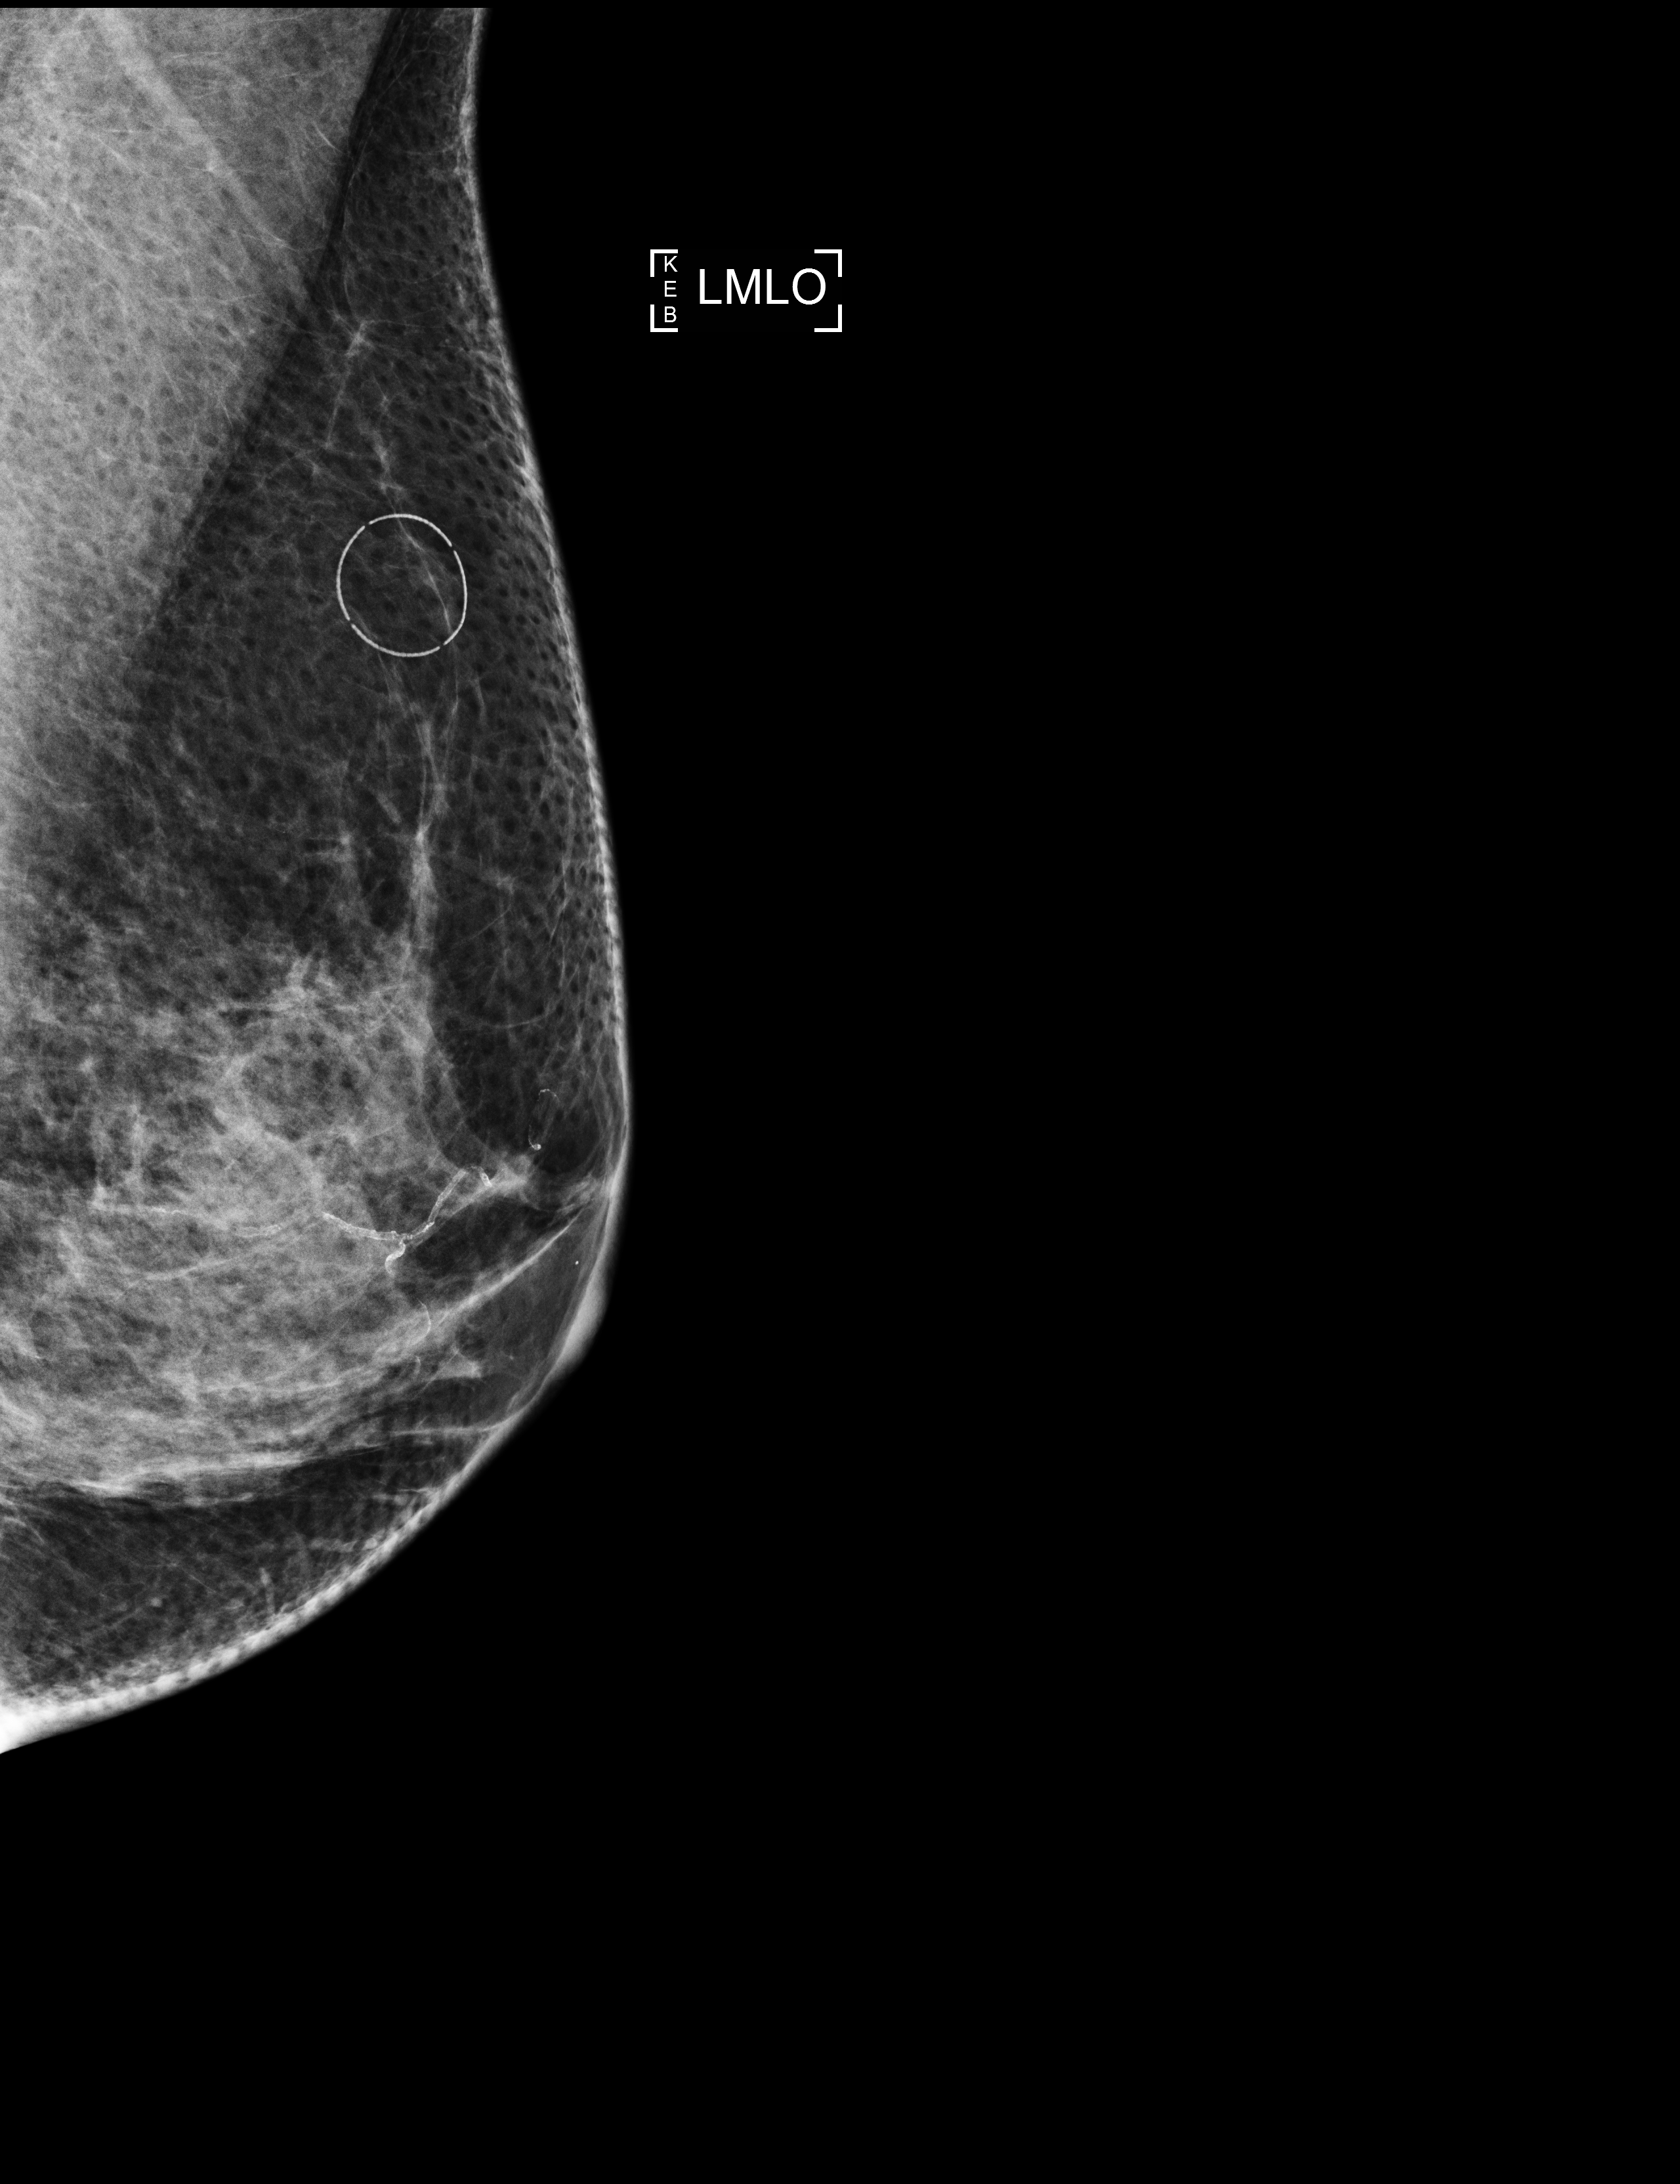
Full-field digital mammogram (FFDM); left breast; MLO view; screening examination; compressed breast thickness 53 mm; system: Selenia Dimensions. Patient aged 64 years (female).
- BI-RADS breast density category at the screening exam (both breasts, scale 1–4): 4
- final BI-RADS assessment for this screening round (tomosynthesis exam, both breasts): category 1
- recall: no recall after this screen